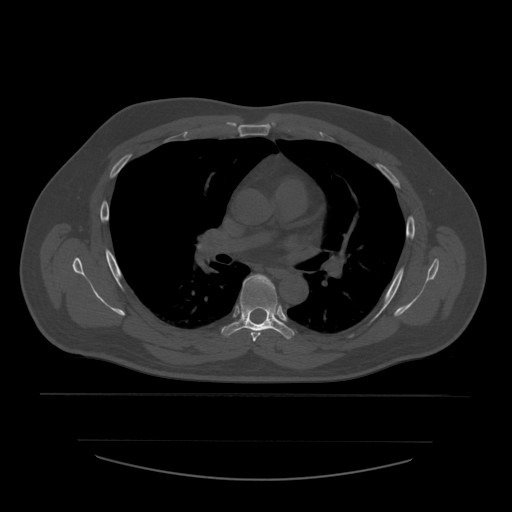
CT including the spine, one axial slice; position 383 of 532 along the scan axis; bone window (W 1800 / L 400 HU); 512 × 512 image matrix. Patient age 44 years. Case-level facts recorded for this patient, not image findings: primary cancer: soft tissue sarcoma.
Annotated regions visible in this slice (semi-automatic segmentation, software-assisted and operator-edited):
- T5 vertebra: bounding box <251,330,264,342> (left, top, right, bottom; pixels)
- T6 vertebra: <222,275,295,340>